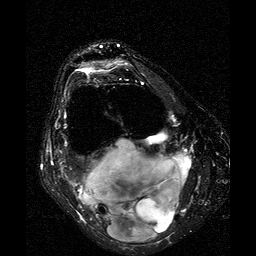
MRI of an extremity soft-tissue mass, one axial slice. Slice 14 of 25 in the series (ordered by position). T2-weighted fat-saturated. 256 × 256 image matrix, field of view 160 × 160 mm. Female patient. From the clinical record (not read from this slice): histological type: liposarcoma; site of the primary tumour: right thigh.
Outlined on this slice (outlined manually by an expert reader):
- gross tumour volume (mass): bounding box (x1, y1, x2, y2) in pixels: (78, 139, 192, 243)